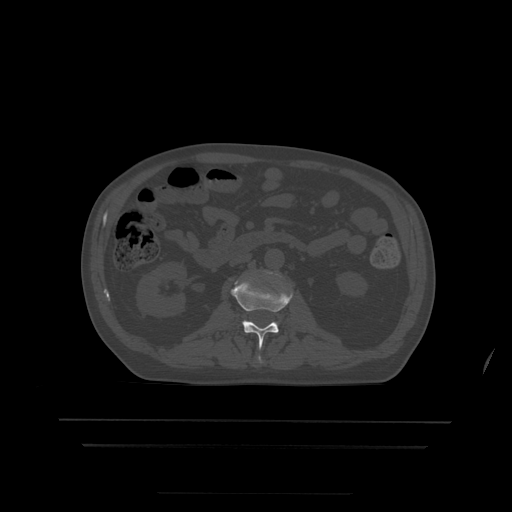
CT including the spine, one axial slice. Slice 141 of 522 in the series (ordered by position). Bone window (W 1800 / L 400 HU). 1.25 mm slice thickness. 512 × 512 image matrix, field of view 436 × 436 mm. Patient age 68 years. From the clinical record (not read from this slice): primary cancer: urothelial.
Structures marked on this image (semi-automatically segmented with operator editing):
- L2 vertebra: bounding box [x1, y1, x2, y2] px = [231, 278, 293, 362]